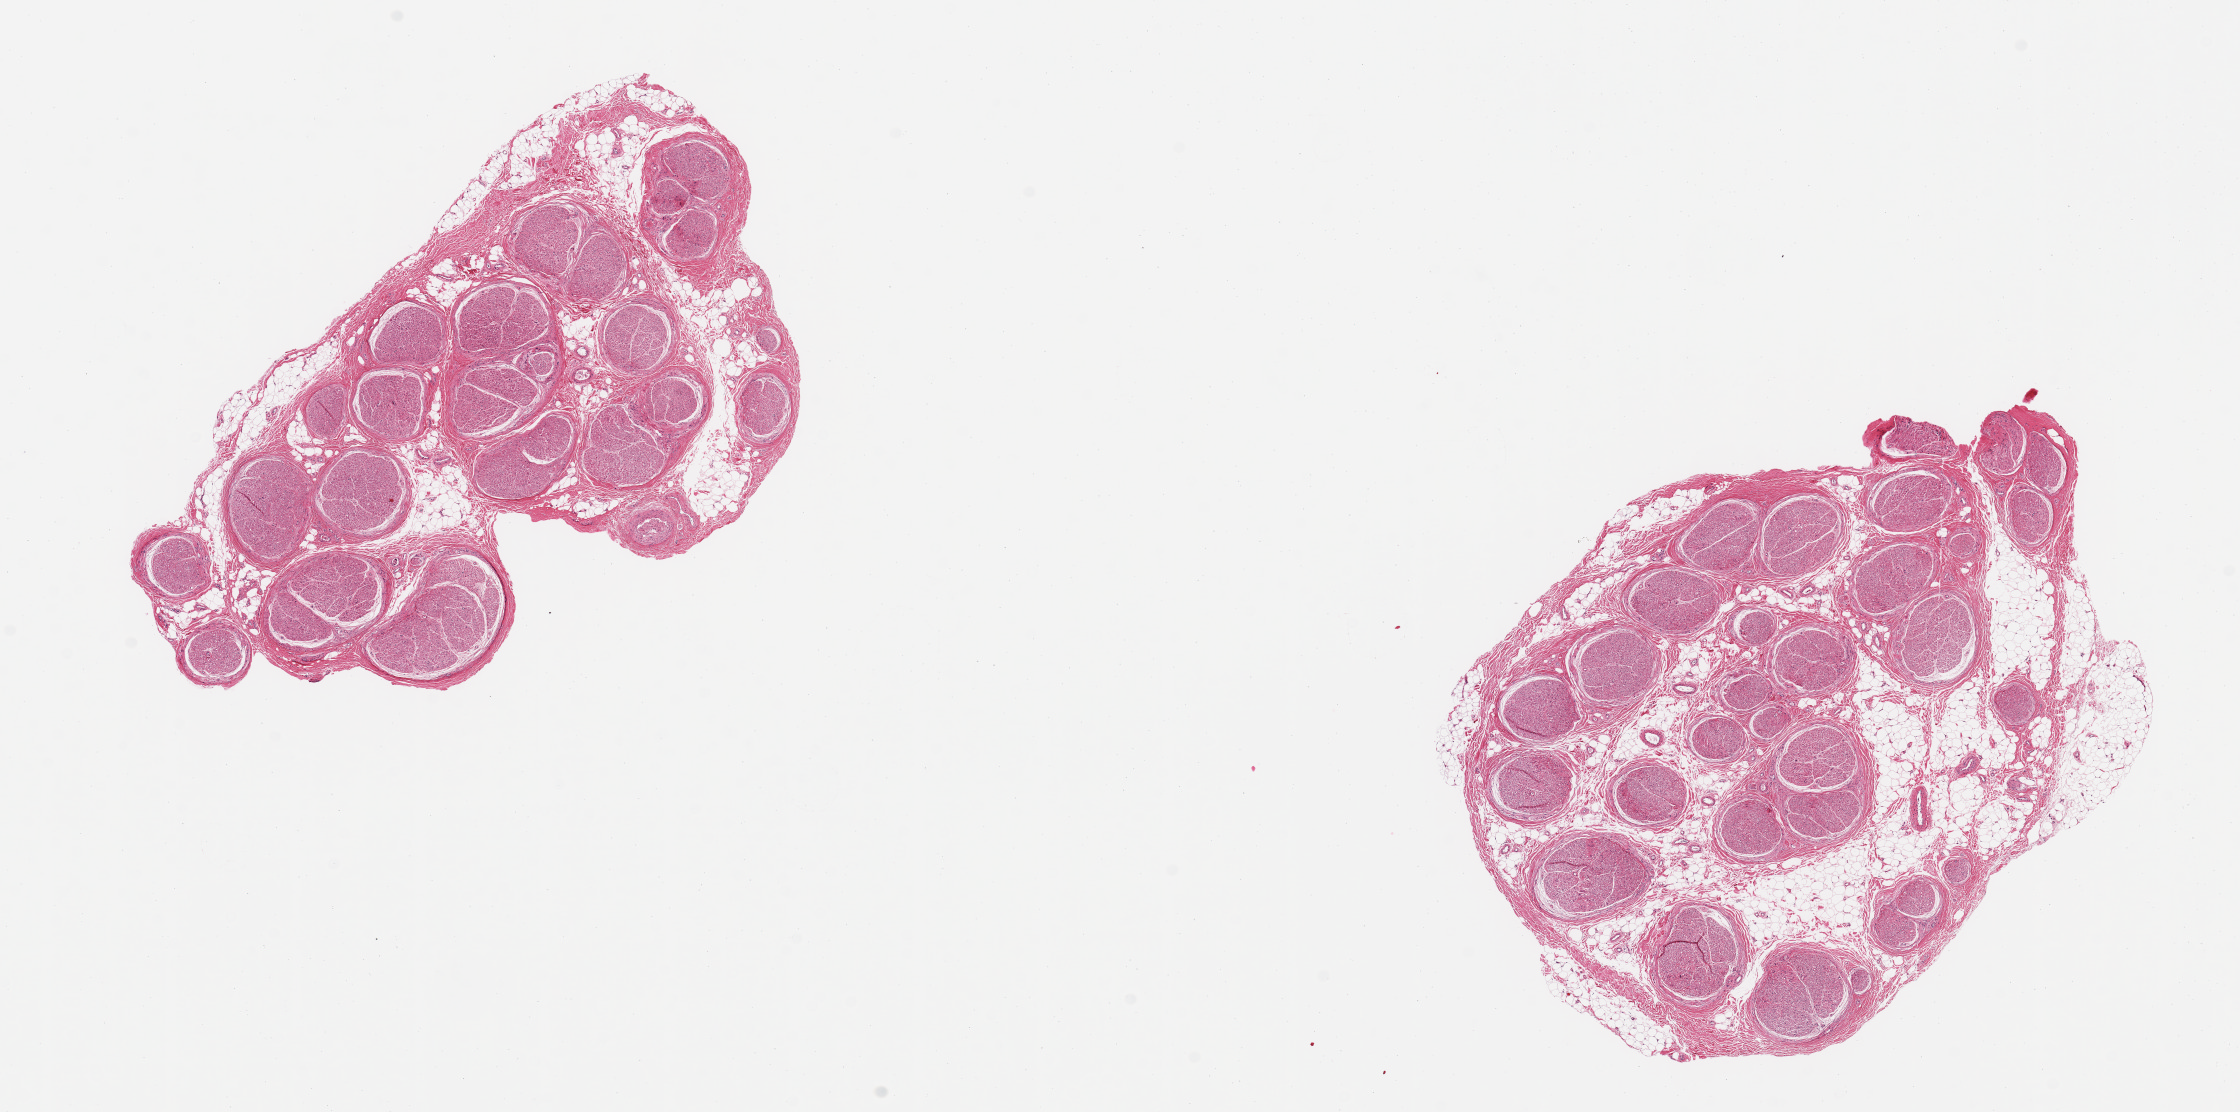
Digitized hematoxylin and eosin (H&E)-stained section, brightfield, a low-resolution overview of the entire scanned area, about 17.7 x 8.8 mm (from a 20x scan), PAXgene-fixed, paraffin-embedded tissue, sampled site (target tissue): tibial nerve, tissue donor sample.
Pathologist's review note for this sample: 2 pieces; 10% and 20% internal/external fat.